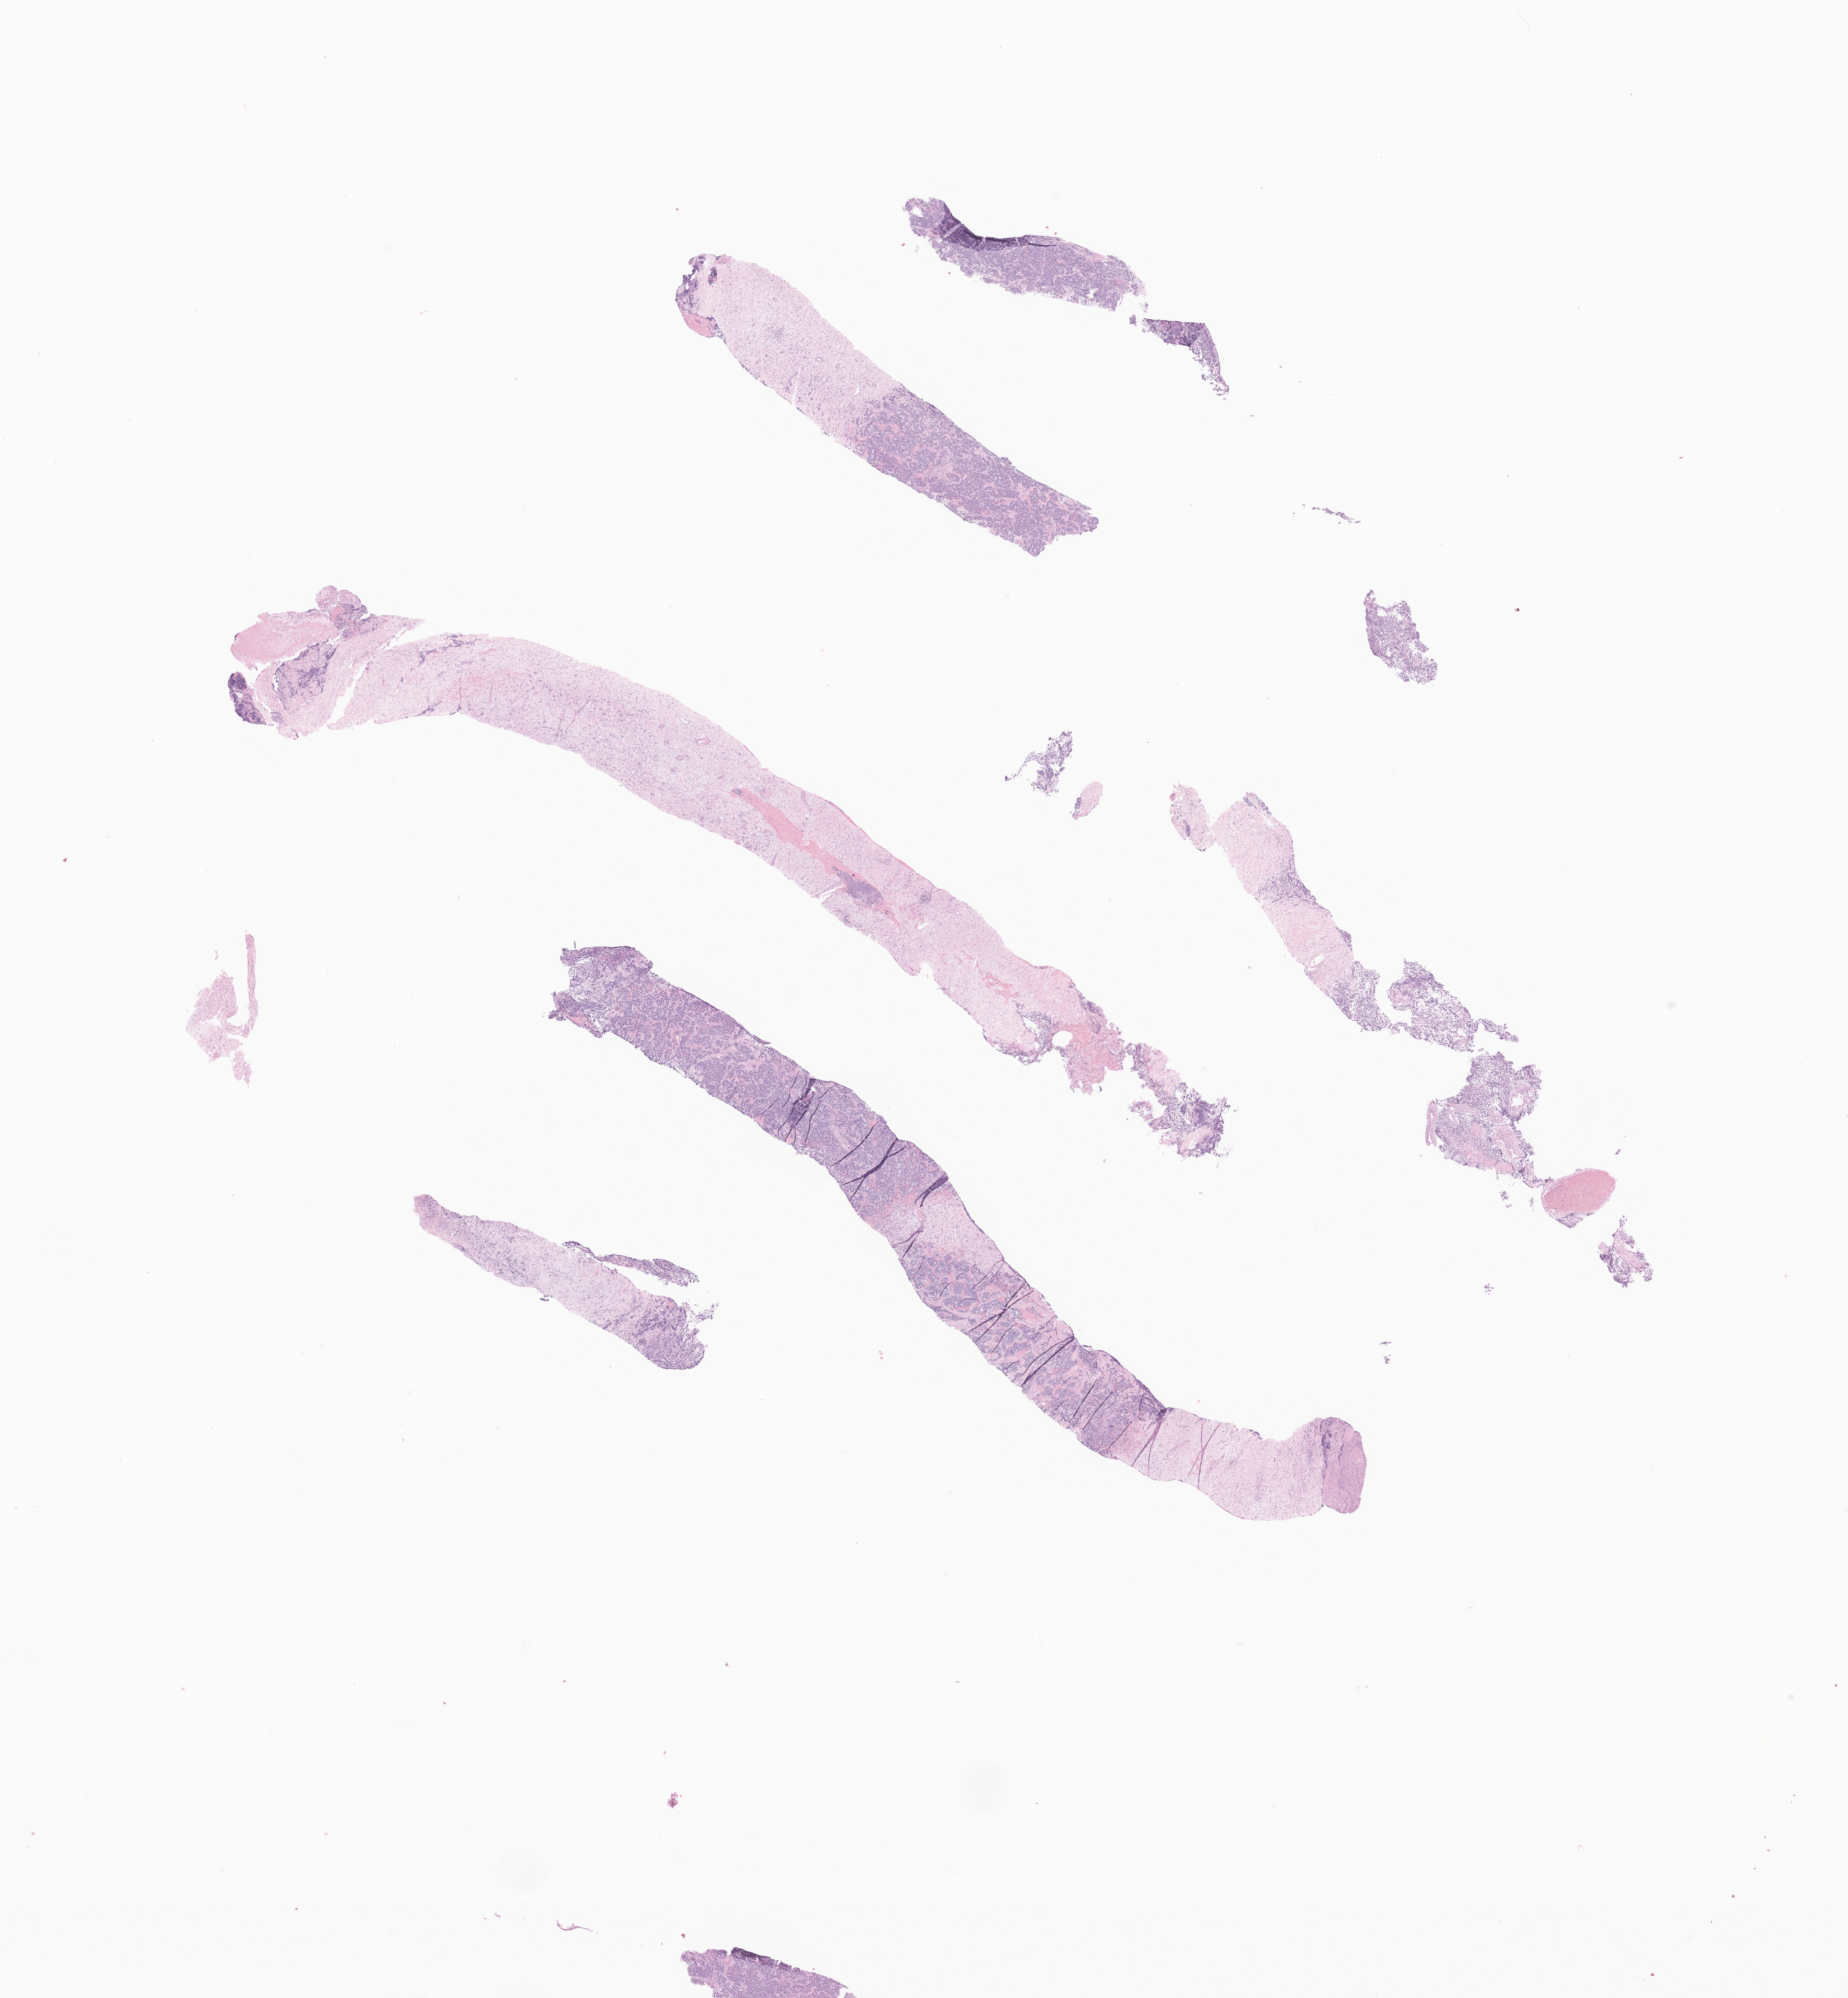
H&E whole-slide image of tumor tissue from the retroperitoneum — a low-resolution overview of the entire scanned area, about 19.2 x 20.7 mm, formalin-fixed paraffin-embedded section. Patient female; age 61 months (5 years 1 month).
• diagnosis (ICD-O-3 morphology term): Ganglioneuroblastoma